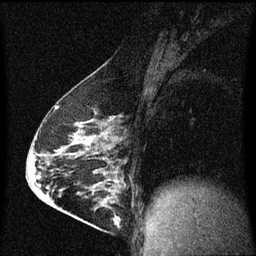
Breast MRI (dynamic contrast-enhanced), one sagittal slice. Slice 35 of 60 in the series (ordered by position). Dynamic contrast-enhanced series, image 2 of 3 at this slice position (ordered by acquisition). 1.5 T. TE 4.2 ms, TR 8 ms. 2 mm slice thickness. 256 × 256 image matrix, field of view 200 × 200 mm. Patient: female, 63 years.
Annotated regions visible in this slice (semi-automatically segmented with operator editing):
- analysis volume of interest (the breast-tissue region the enhancement analysis was run in; not a lesion): box from (x=88, y=182) to (x=127, y=229) px
- tumour enhancement mask (voxels above the 70 % enhancement threshold inside the analysis volume of interest): (x=96, y=182)–(x=121, y=227)